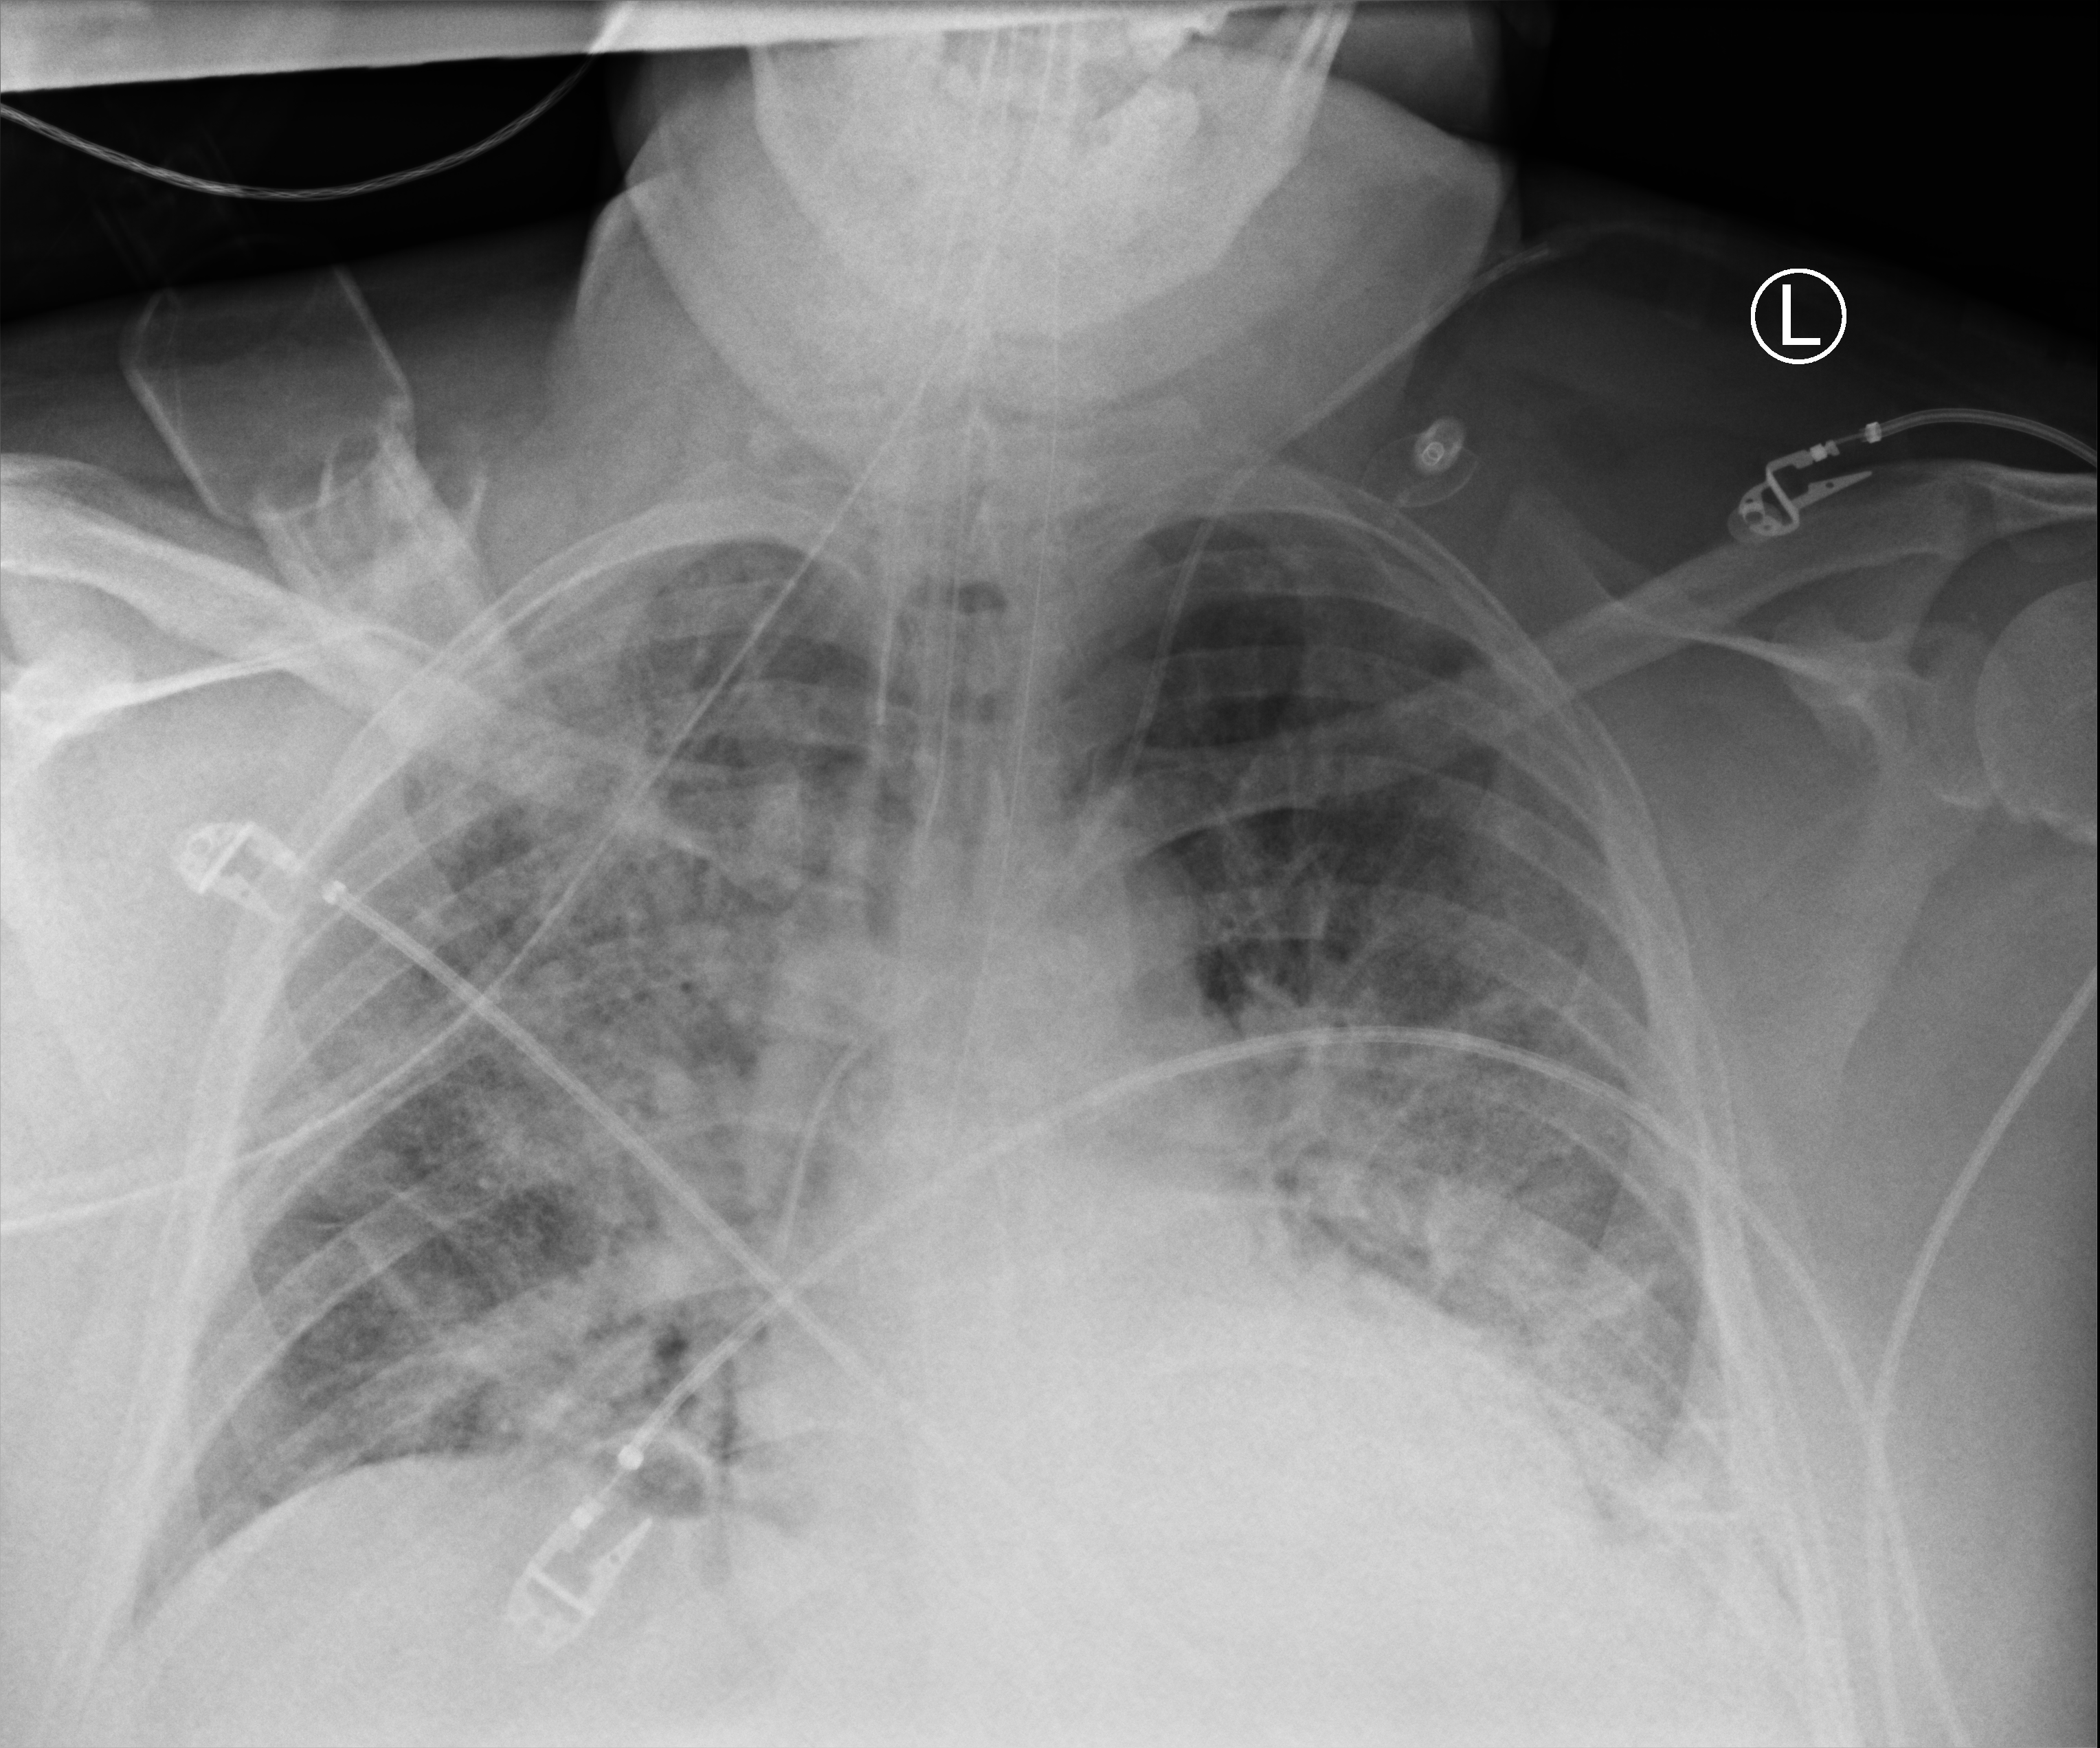
Portable chest radiograph, anteroposterior (AP) projection. Patient hospitalised with COVID-19, aged 18–59 years.
Admission-level facts for this patient (not findings on this image; timing relative to this image not recorded): admitted to intensive care during this hospital stay: yes; mechanically ventilated during this hospital stay: yes; length of hospital stay: 16 days.